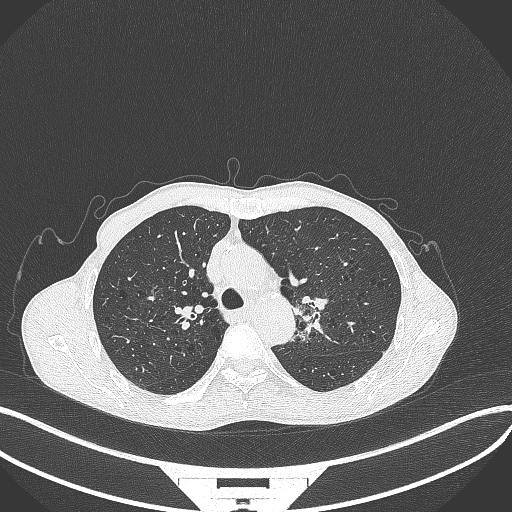
Chest CT, one axial slice. Reconstruction kernel B70f. Lung window (W 1500 / L -600 HU). 1 mm slice thickness. 512 × 512 image matrix. Patient: male, 65 years. From the clinical record (not read from this slice): clinical TNM (as recorded): T2b N0 M0.
Outlined on this slice (bounding box drawn by a radiologist):
- lung tumour (recorded histology: adenocarcinoma): bounding box [x1, y1, x2, y2] px = [287, 287, 333, 350]